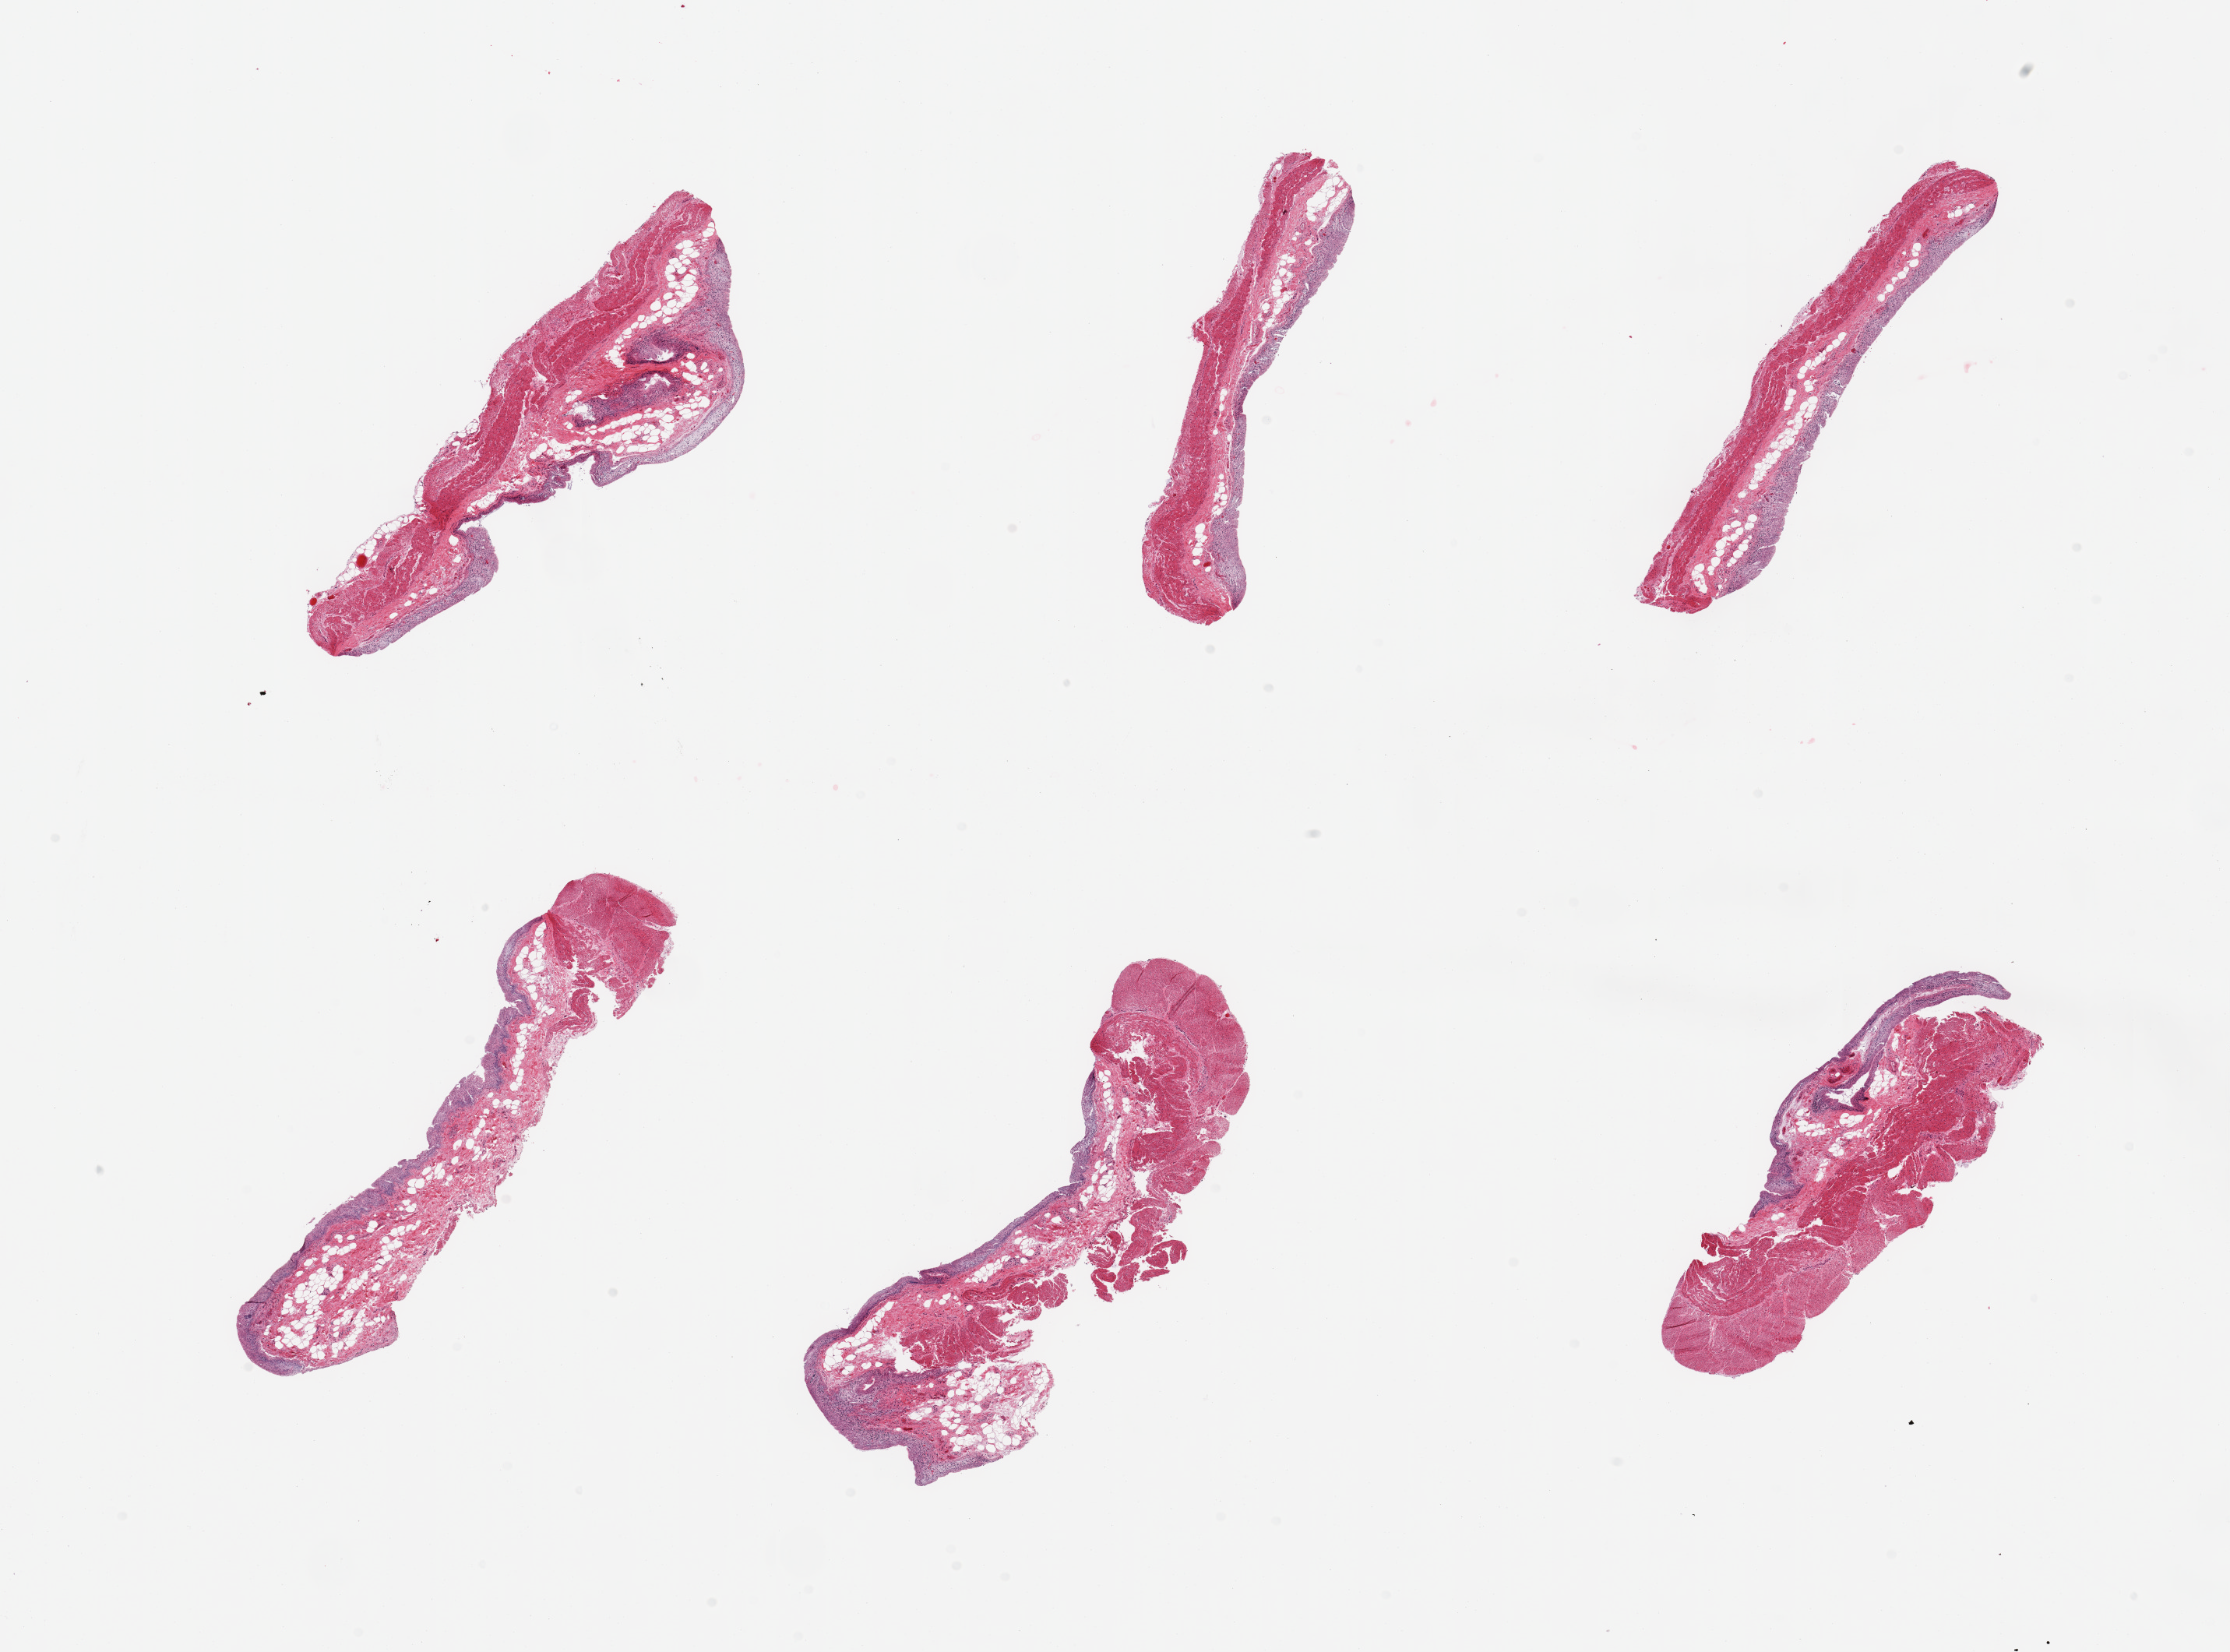
Haematoxylin and eosin whole-slide image, whole scanned area (about 22.6 x 16.8 mm, acquisition: 20x scan) shown as a low-resolution overview, PAXgene-fixed, paraffin-embedded tissue, sampled site (target tissue): transverse colon, tissue donor sample. Donor sex: male.
Pathologist's review note for this sample: 6 pieces, mucosa with advanced autolysis.